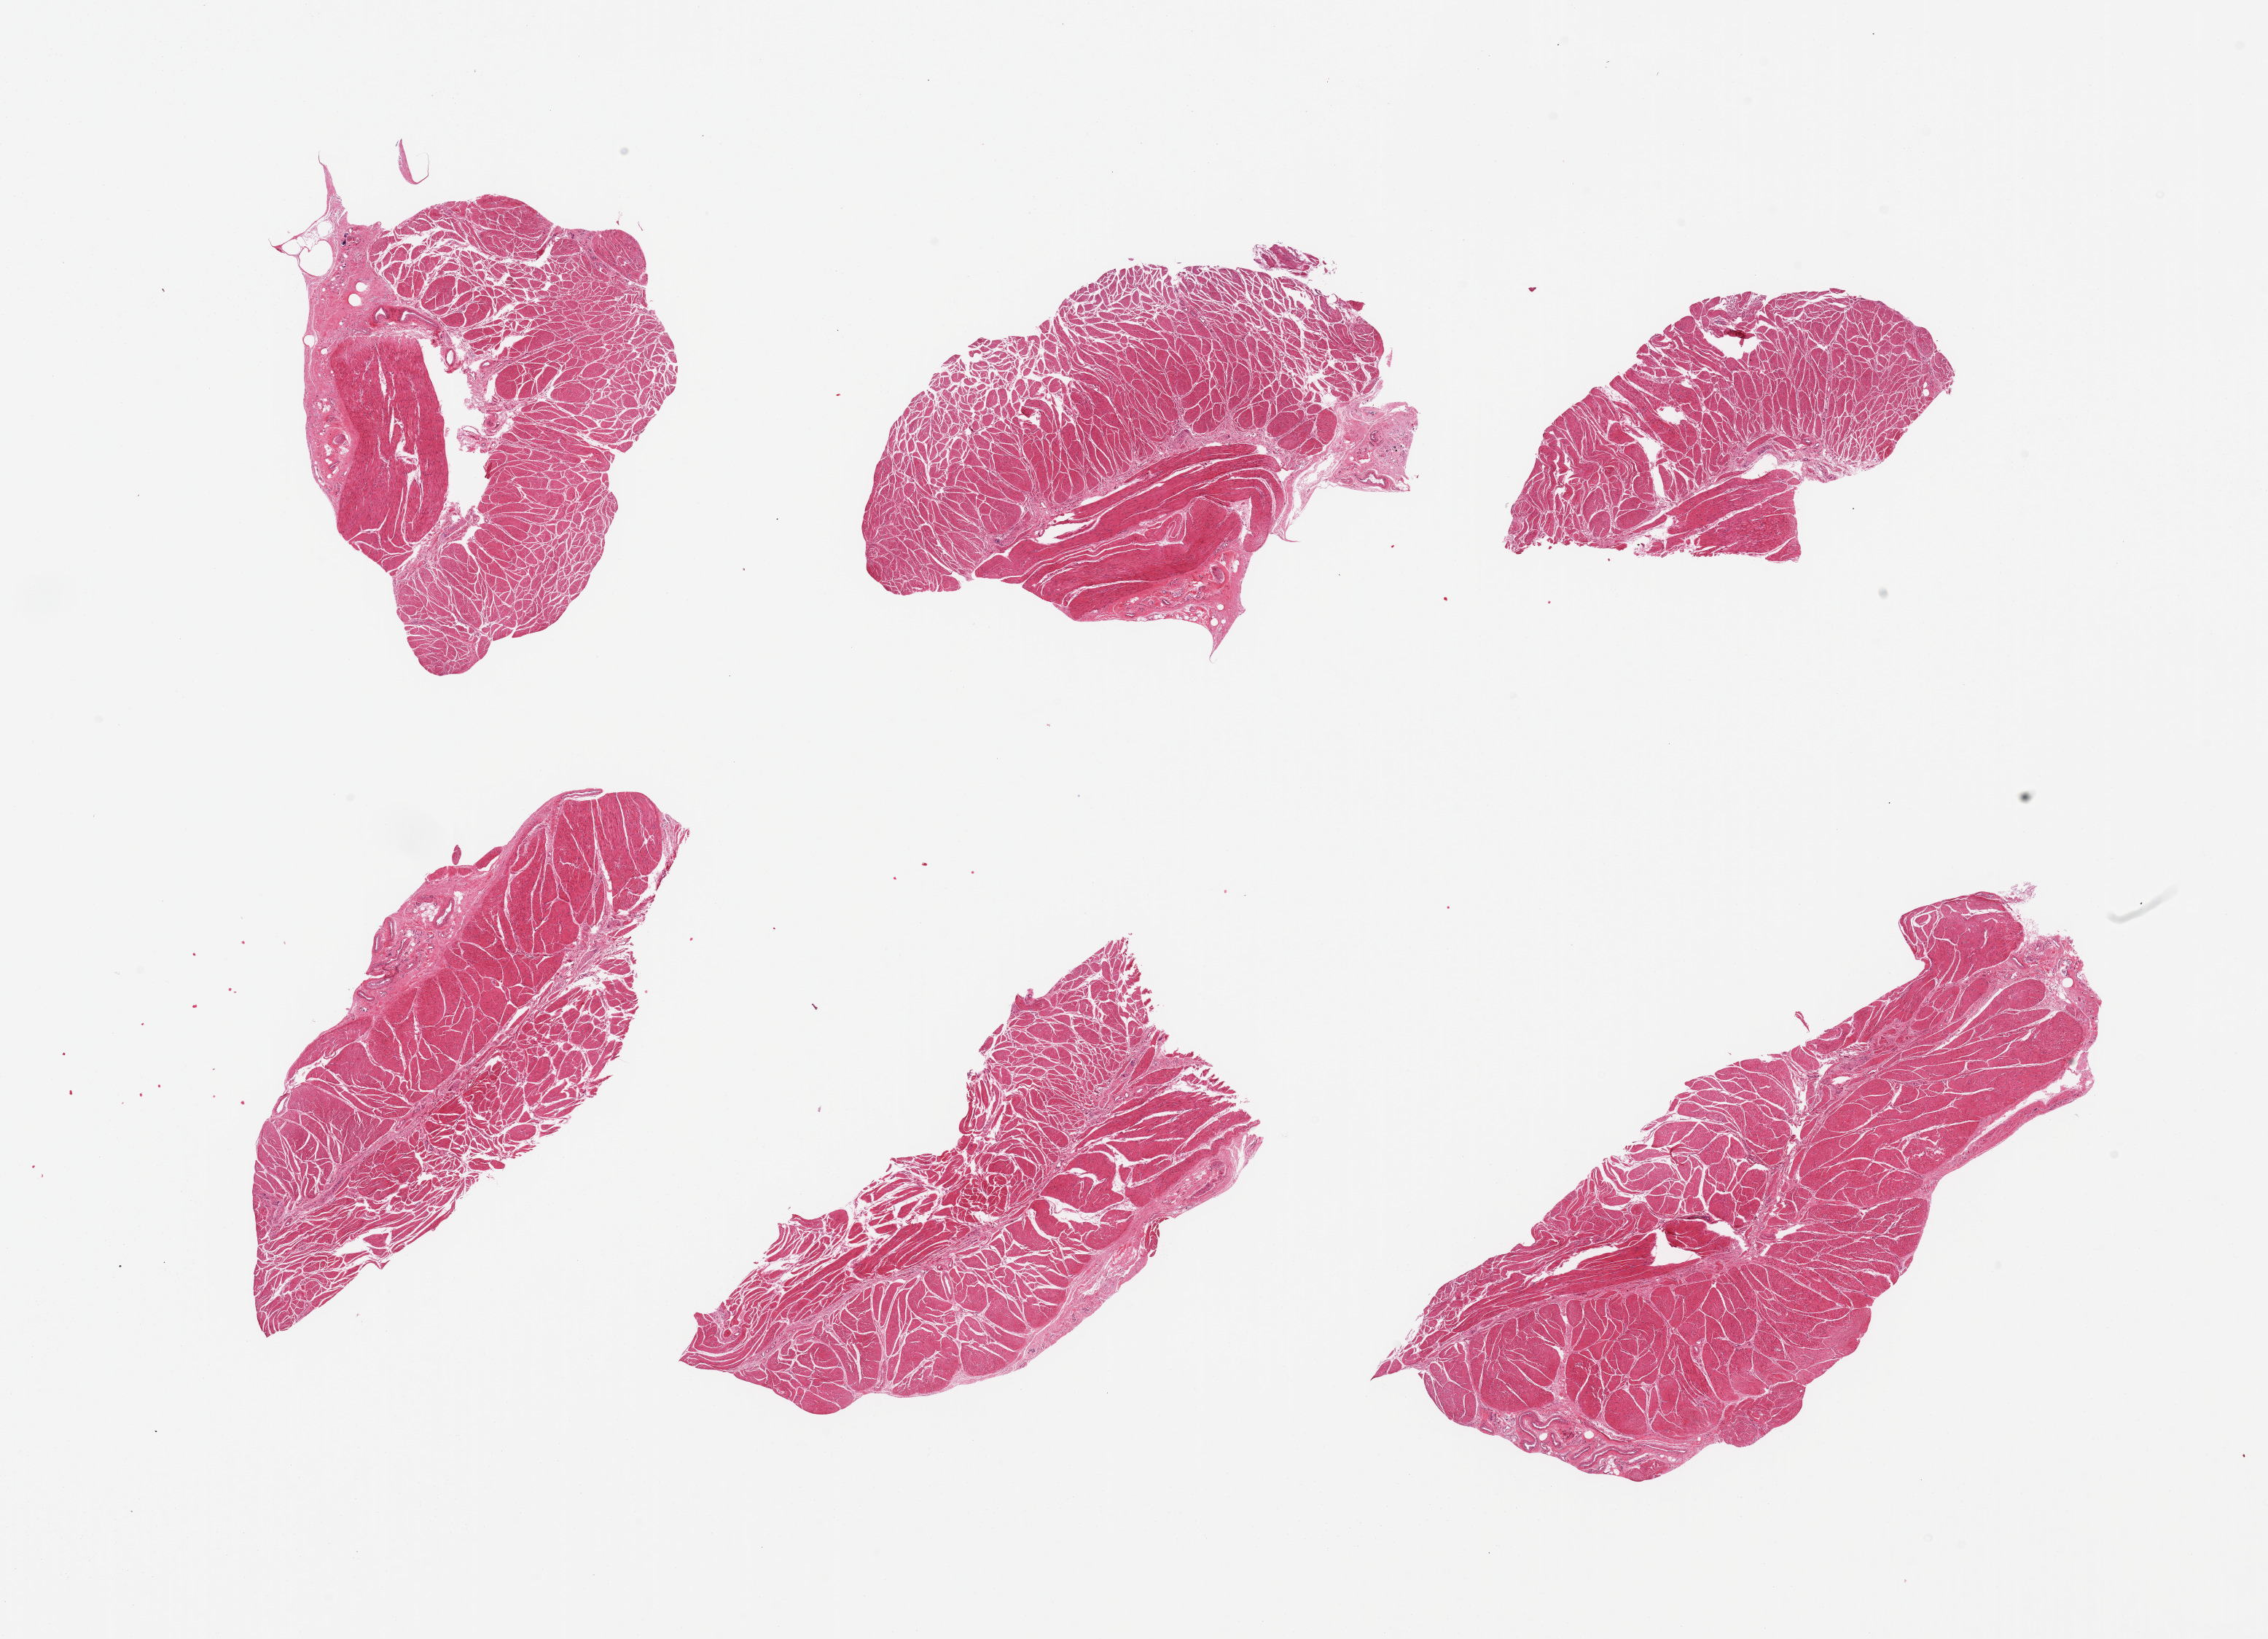
Digitized hematoxylin and eosin (H&E)-stained section, a low-resolution overview of the entire scanned area, about 24.6 x 17.8 mm (acquisition: 20x scan); PAXgene-fixed, paraffin-embedded tissue; section of esophageal muscle (target tissue); donor tissue sample.
Reviewer comment on this tissue sample: 6 pieces, confirmed target muscularis.